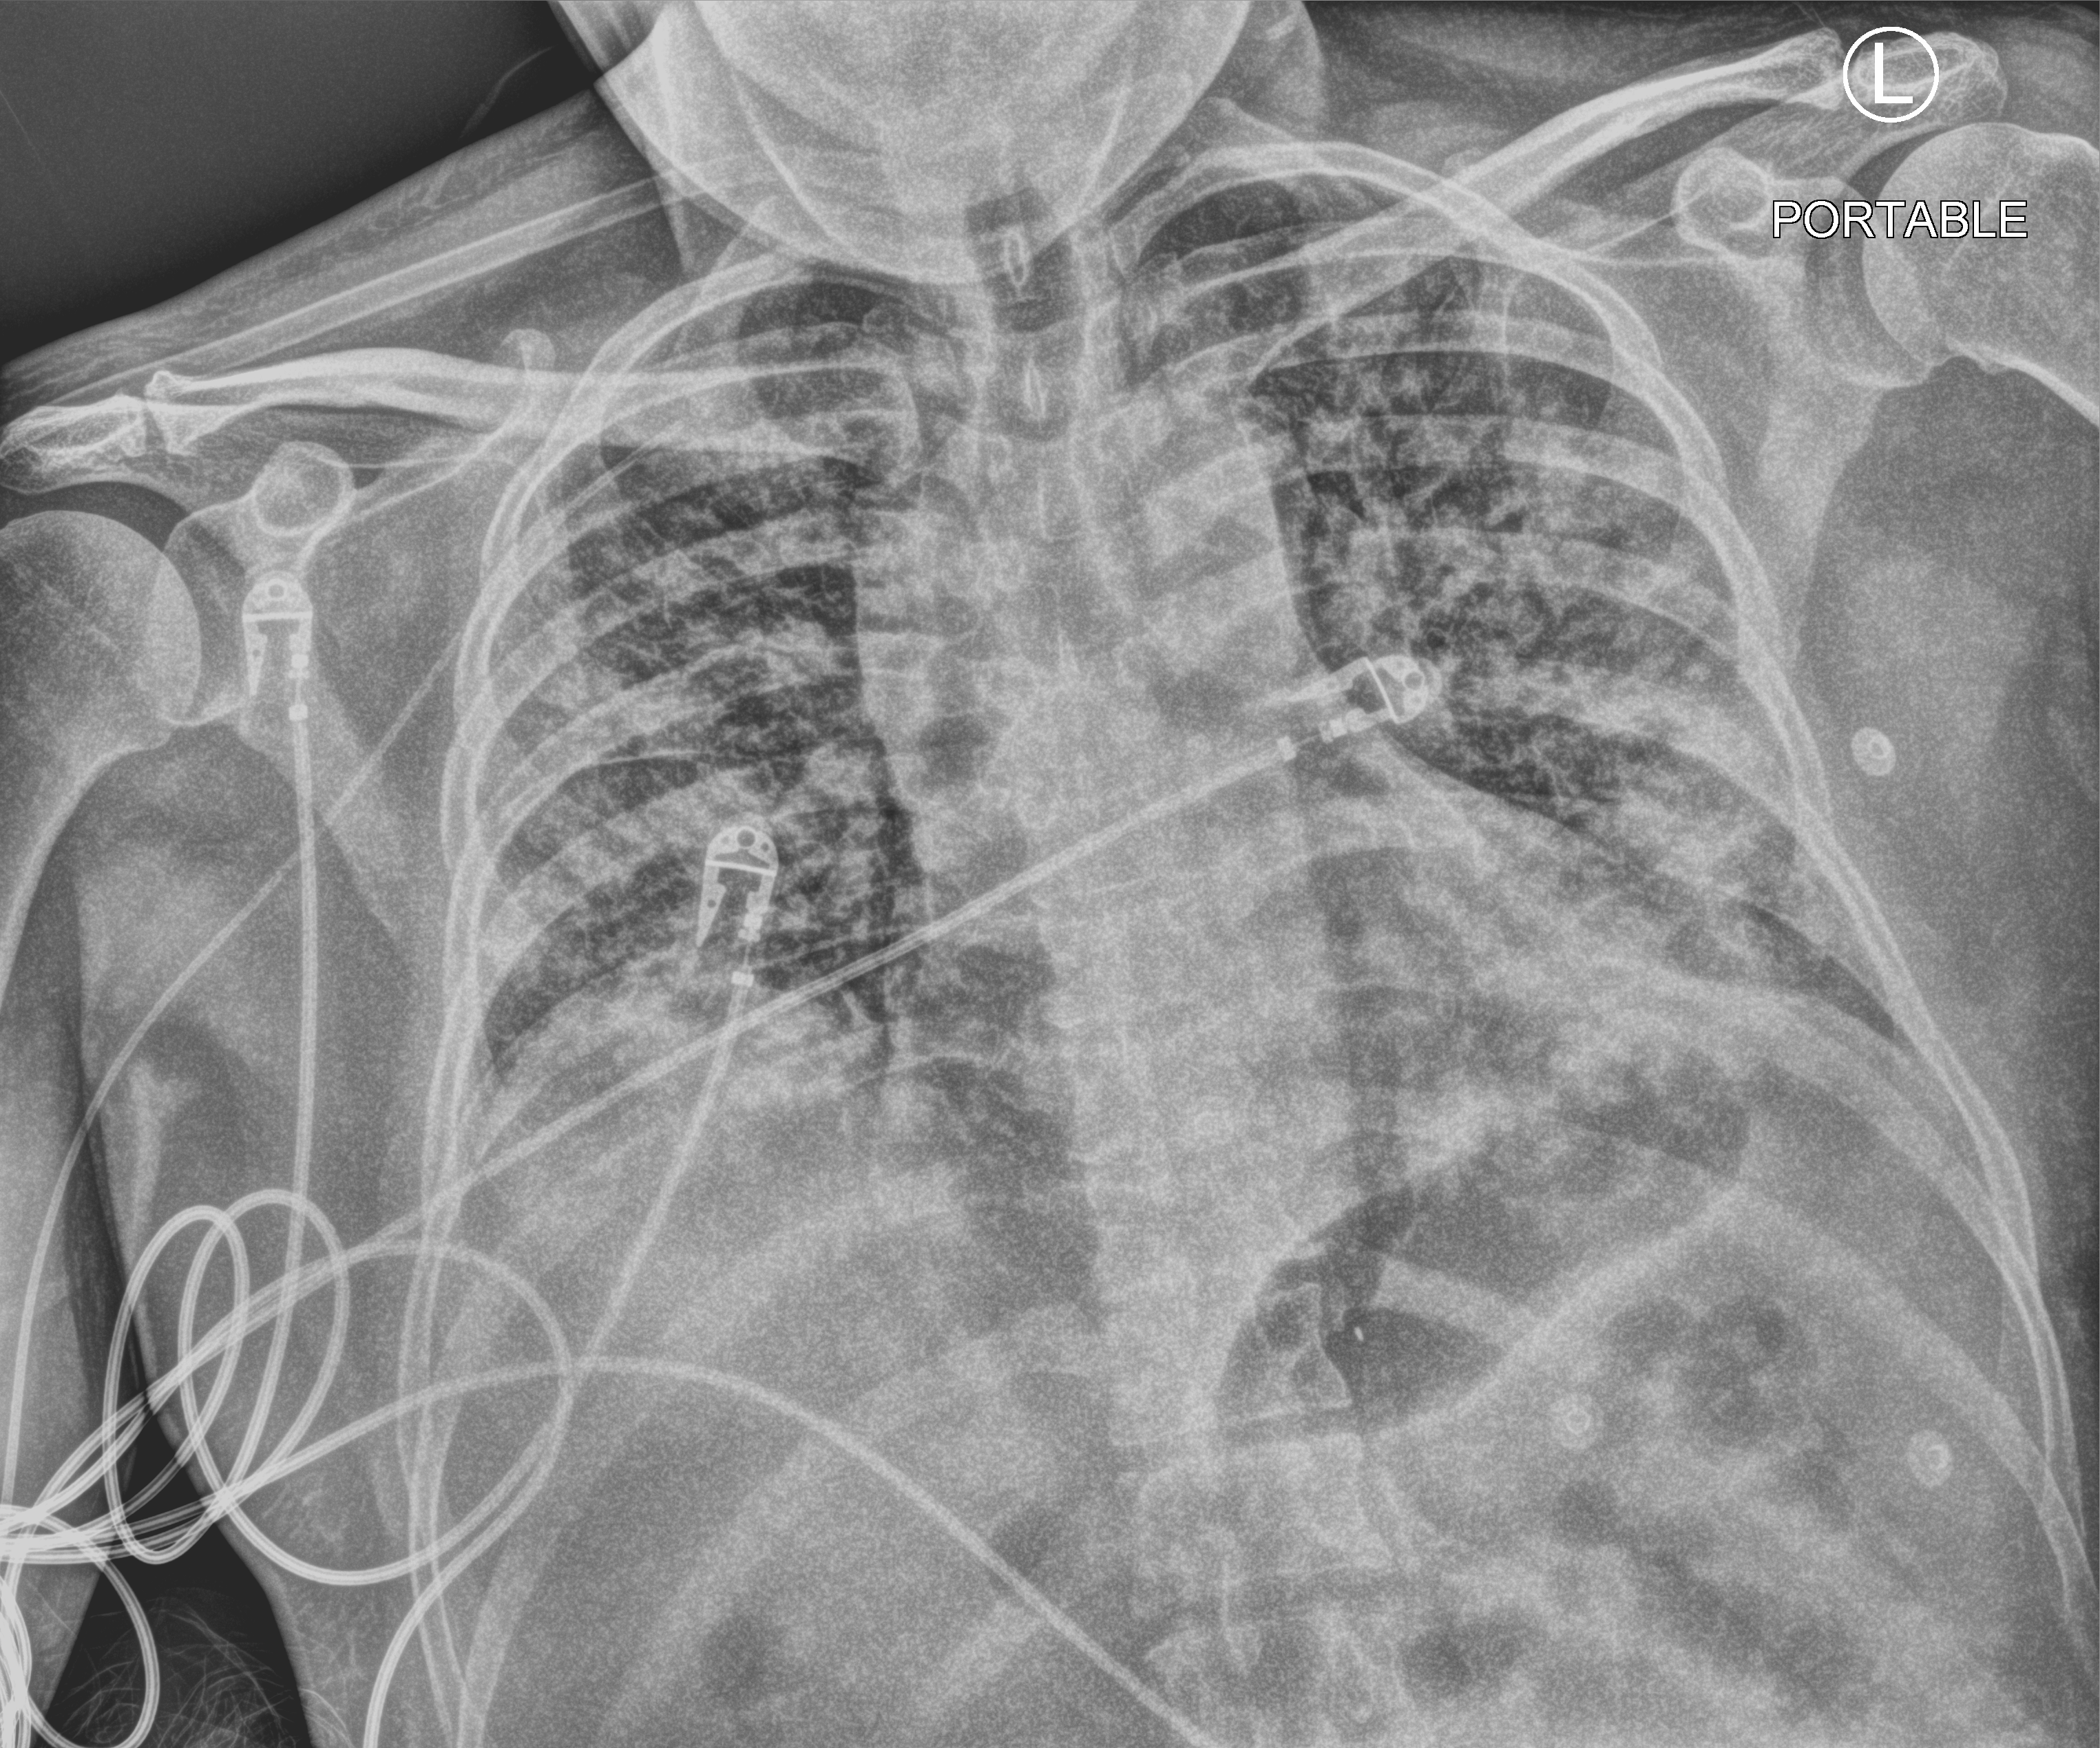
Chest X-ray (portable). Male patient hospitalised with COVID-19, age 18–59 years.
Admission-level facts for this patient (not findings on this image; timing relative to this image not recorded): length of hospital stay: 16 days; COPD (admission record): no.